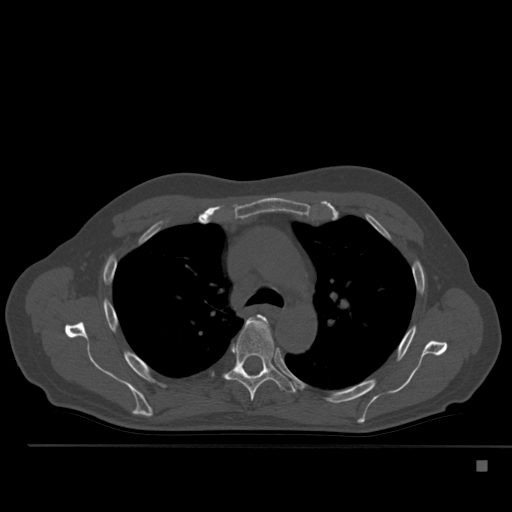
CT including the spine, one axial slice. Position 367 of 517 along the scan axis. Reconstruction kernel Br40s. Bone window (W 1800 / L 400 HU). 512 × 512 image matrix, field of view 408 × 408 mm. Patient: male, 70 years. From the clinical record (not read from this slice): primary cancer: renal.
Structures marked on this image (semi-automatic segmentation, software-assisted and operator-edited):
- T4 vertebra: bounding box [x1, y1, x2, y2] px = [262, 317, 266, 320]
- T5 vertebra: [224, 318, 295, 401]